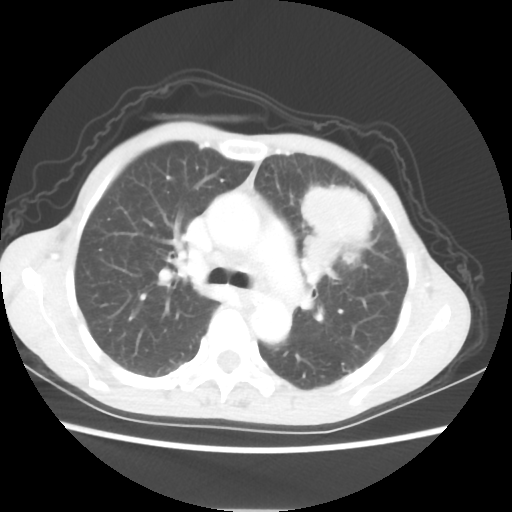
Chest CT, one axial slice; position 39 of 56 along the scan axis; lung window (W 1500 / L -600 HU); 5 mm slice thickness; 512 × 512 image matrix, field of view 331 × 331 mm. Female patient, age 60 years. Case-level facts recorded for this patient, not image findings: clinical TNM (as recorded): T4 N1 M0.
Annotated regions visible in this slice (bounding box drawn by a radiologist):
- lung tumour (recorded histology: adenocarcinoma): bounding box (x1, y1, x2, y2) in pixels: (296, 184, 372, 292)